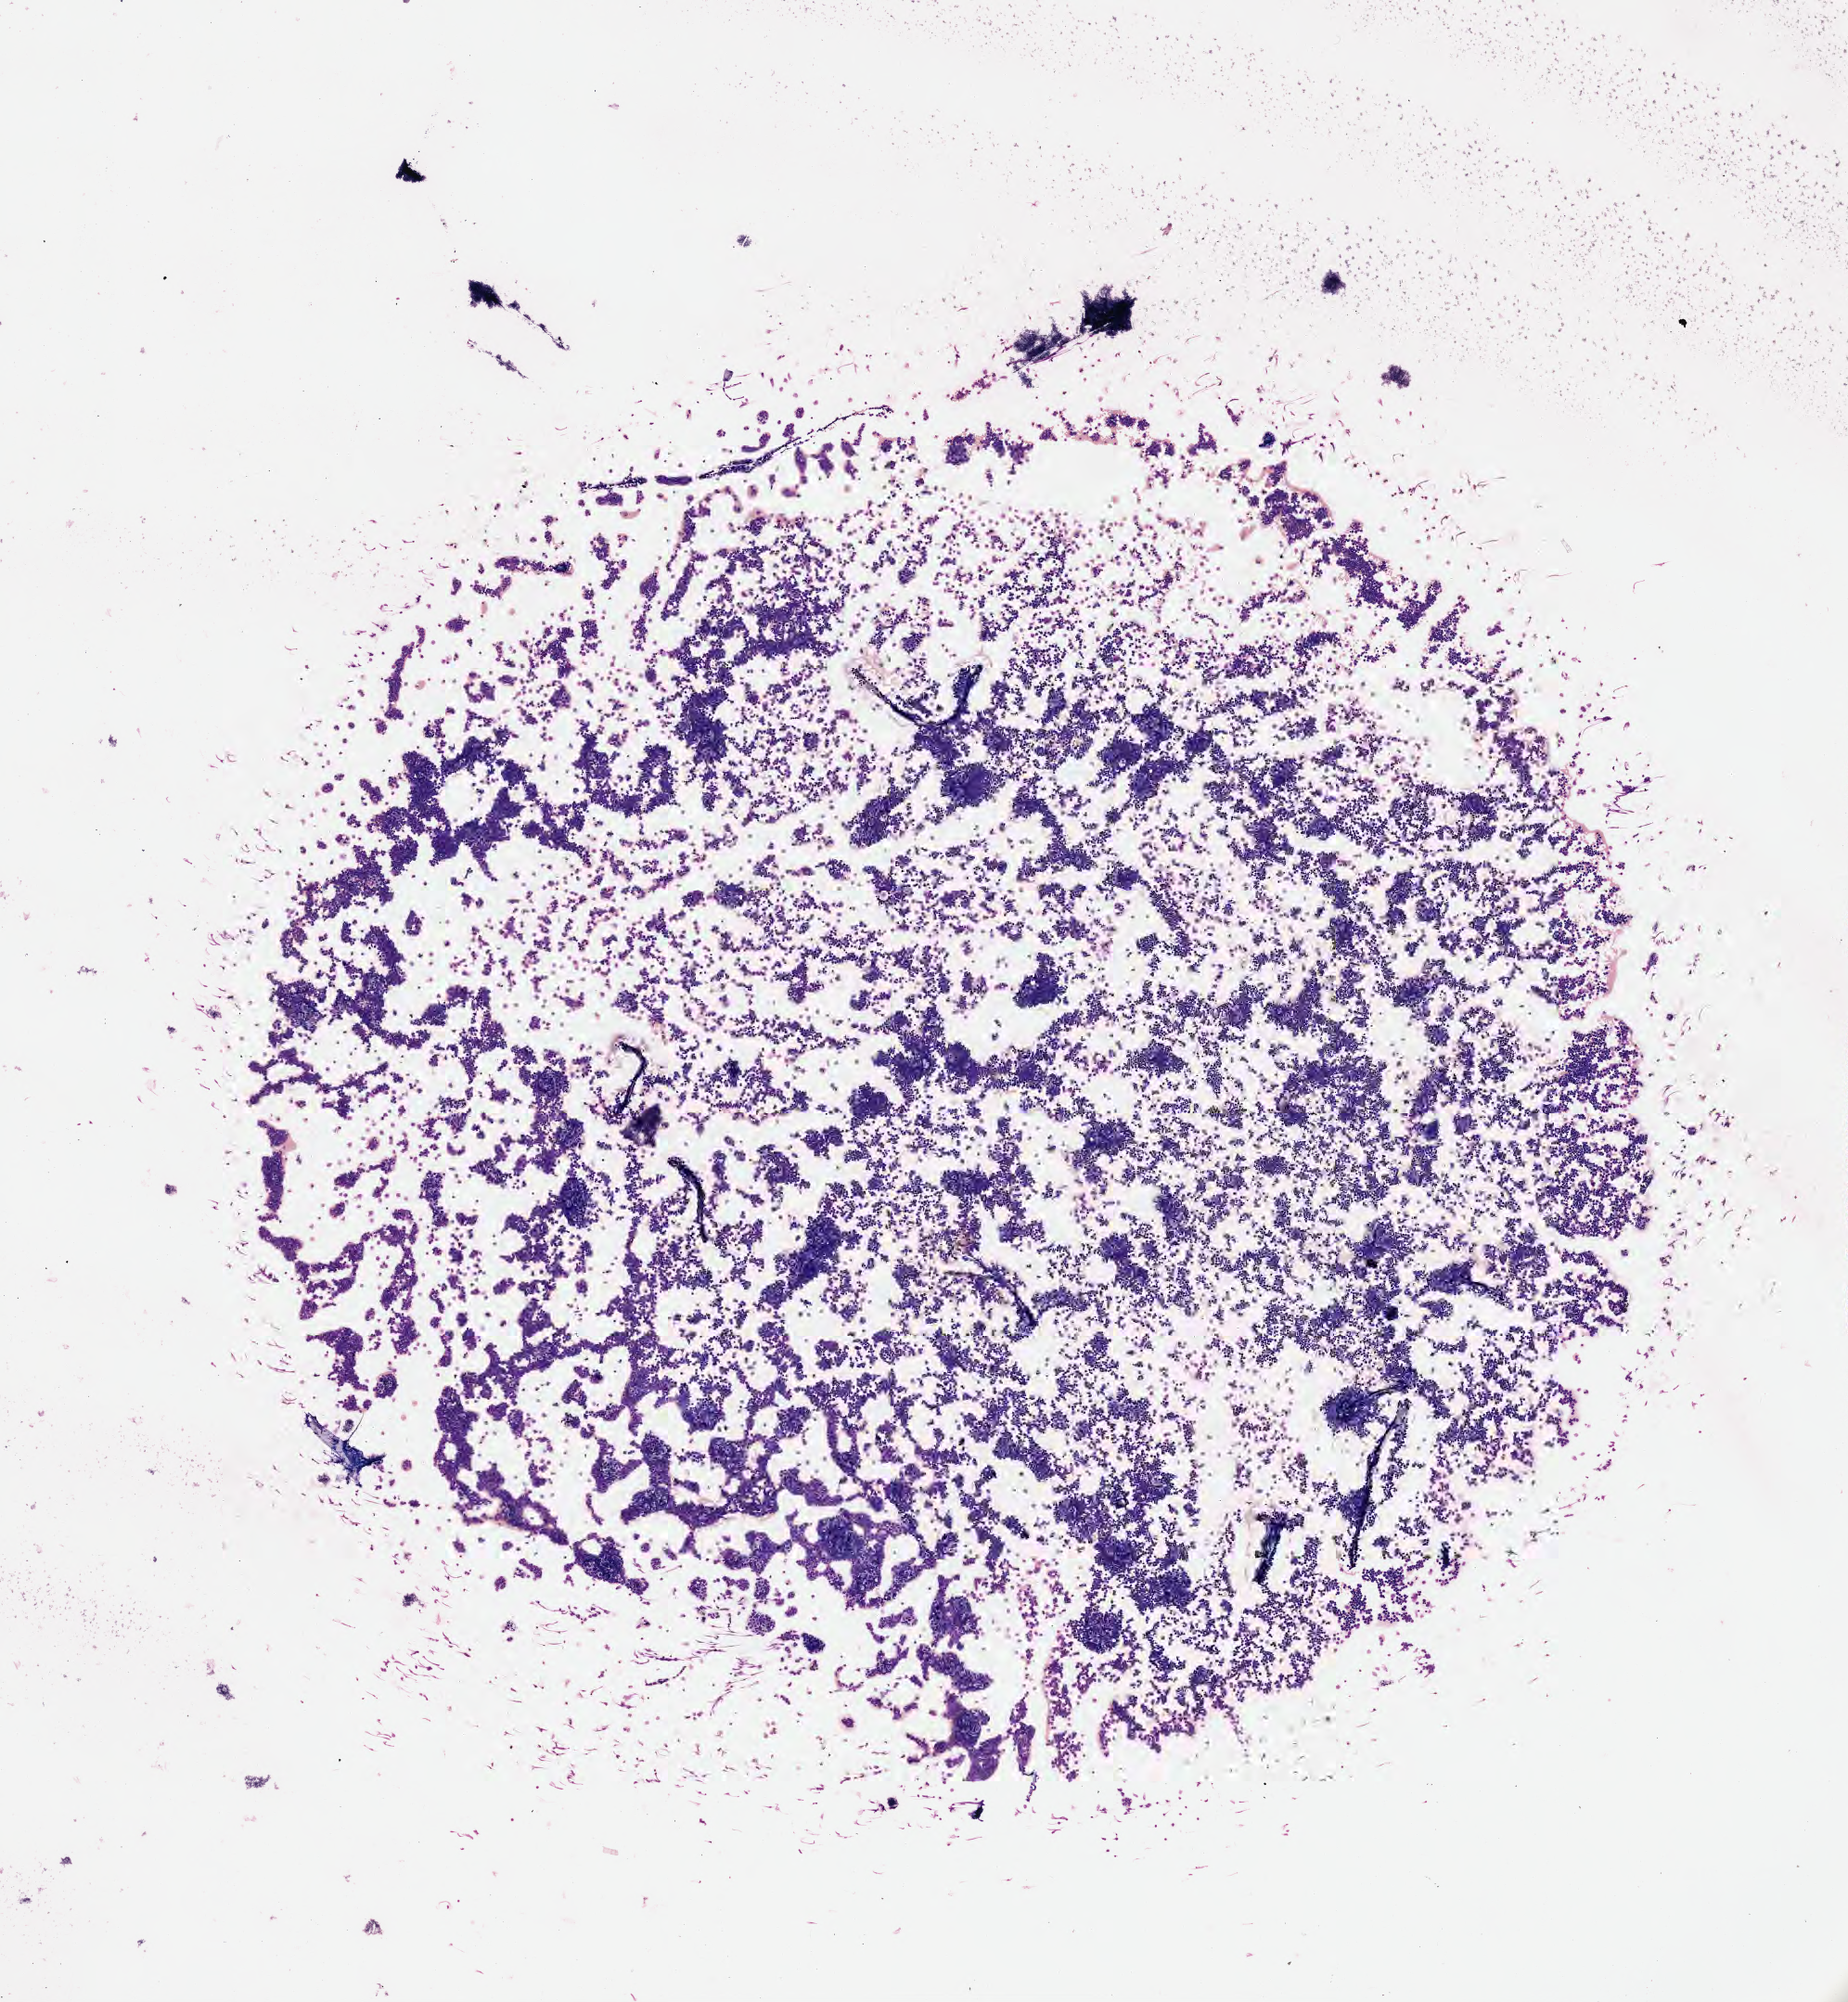
Whole-slide image, Wright-Giemsa stain, low-resolution overview of the scanned area, about 8.0 x 8.7 mm, specimen: tumor tissue, anatomic site: pleura. Female, age 3 years at initial diagnosis.
Histologic diagnosis: Malignant lymphoma, non-Hodgkin, NOS.